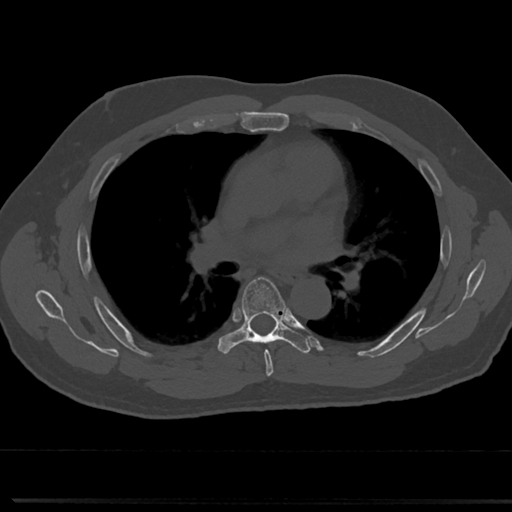
CT including the spine, one axial slice. Slice 463 of 817 in the series (ordered by position). Reconstruction kernel Br40s/3. 120 kVp. Bone window (W 1800 / L 400 HU). 0.5 mm slice thickness. 512 × 512 image matrix. Male patient, age 61 years. From the clinical record (not read from this slice): primary cancer: prostate.
Annotated regions visible in this slice (semi-automatic segmentation, software-assisted and operator-edited):
- T5 vertebra: box from (x=247, y=333) to (x=274, y=367) px
- T6 vertebra: (x=217, y=275)–(x=309, y=355)